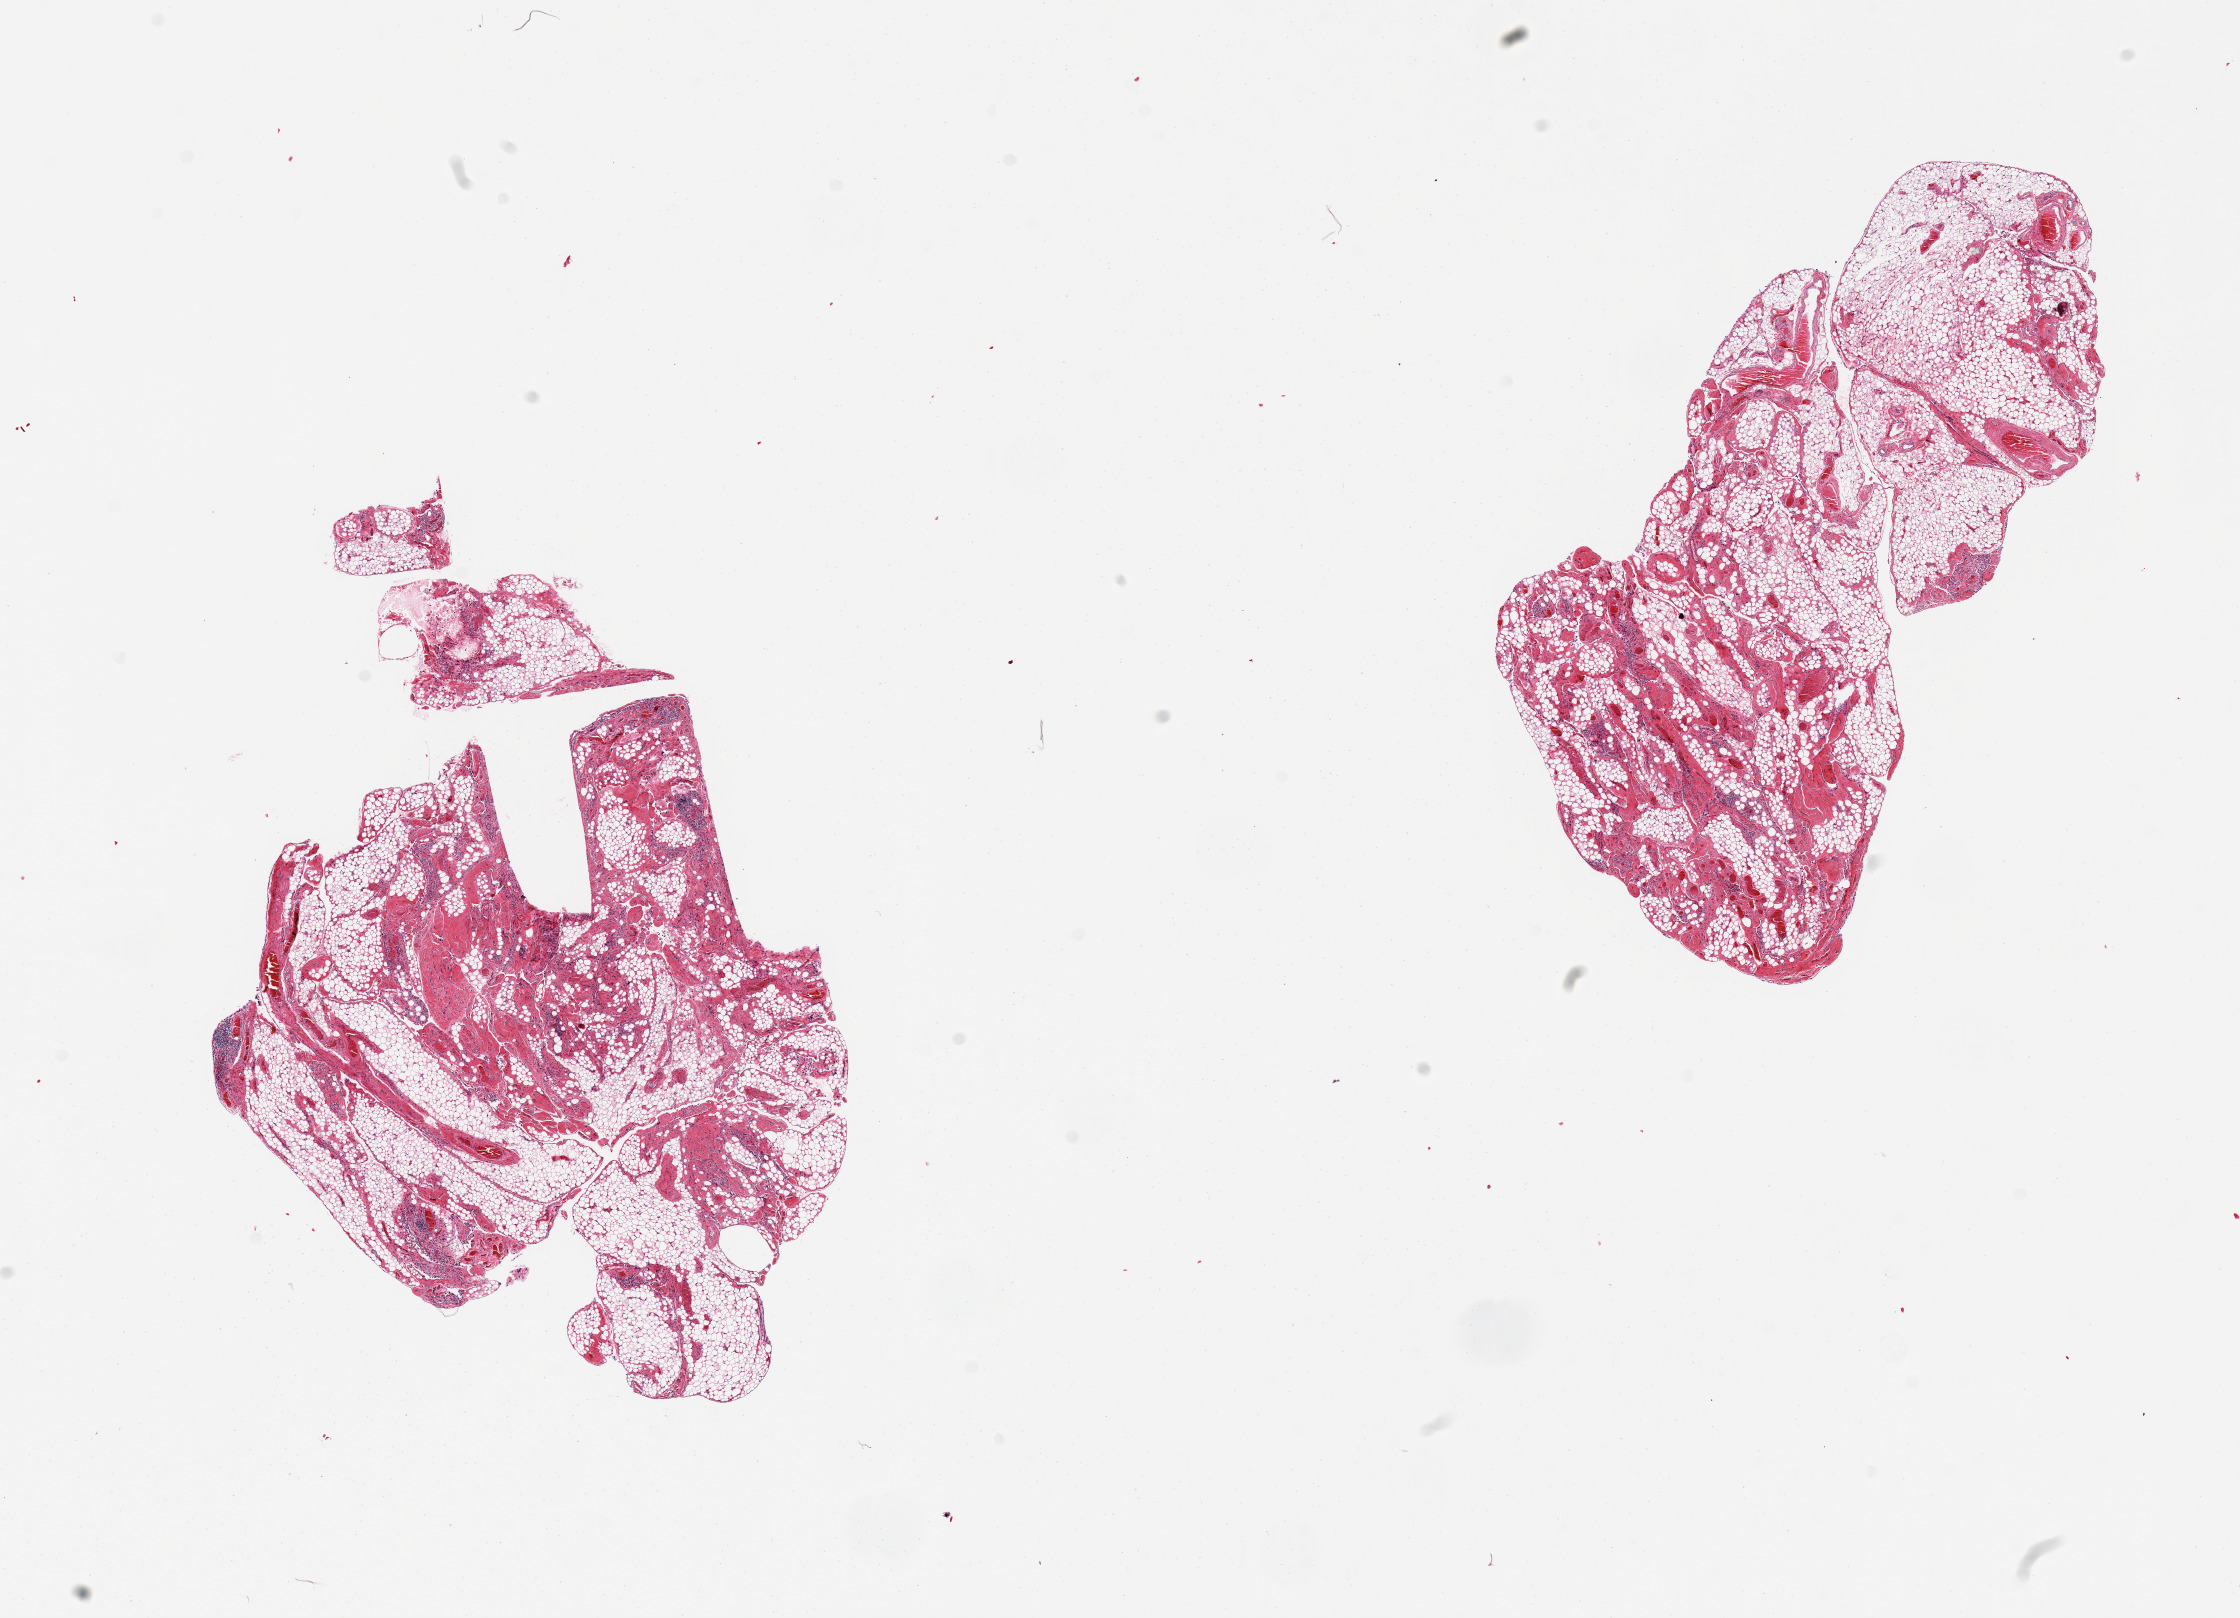
Digitized haematoxylin and eosin-stained section — whole scanned area (about 17.7 x 12.8 mm) shown as a low-resolution overview, PAXgene-fixed, paraffin-embedded tissue, section of omentum (target tissue), tissue donor sample. Male donor.
Review note (as recorded): 2 pieces, ~50% fibrous and vascular tissue with chronic inflammatory cells.